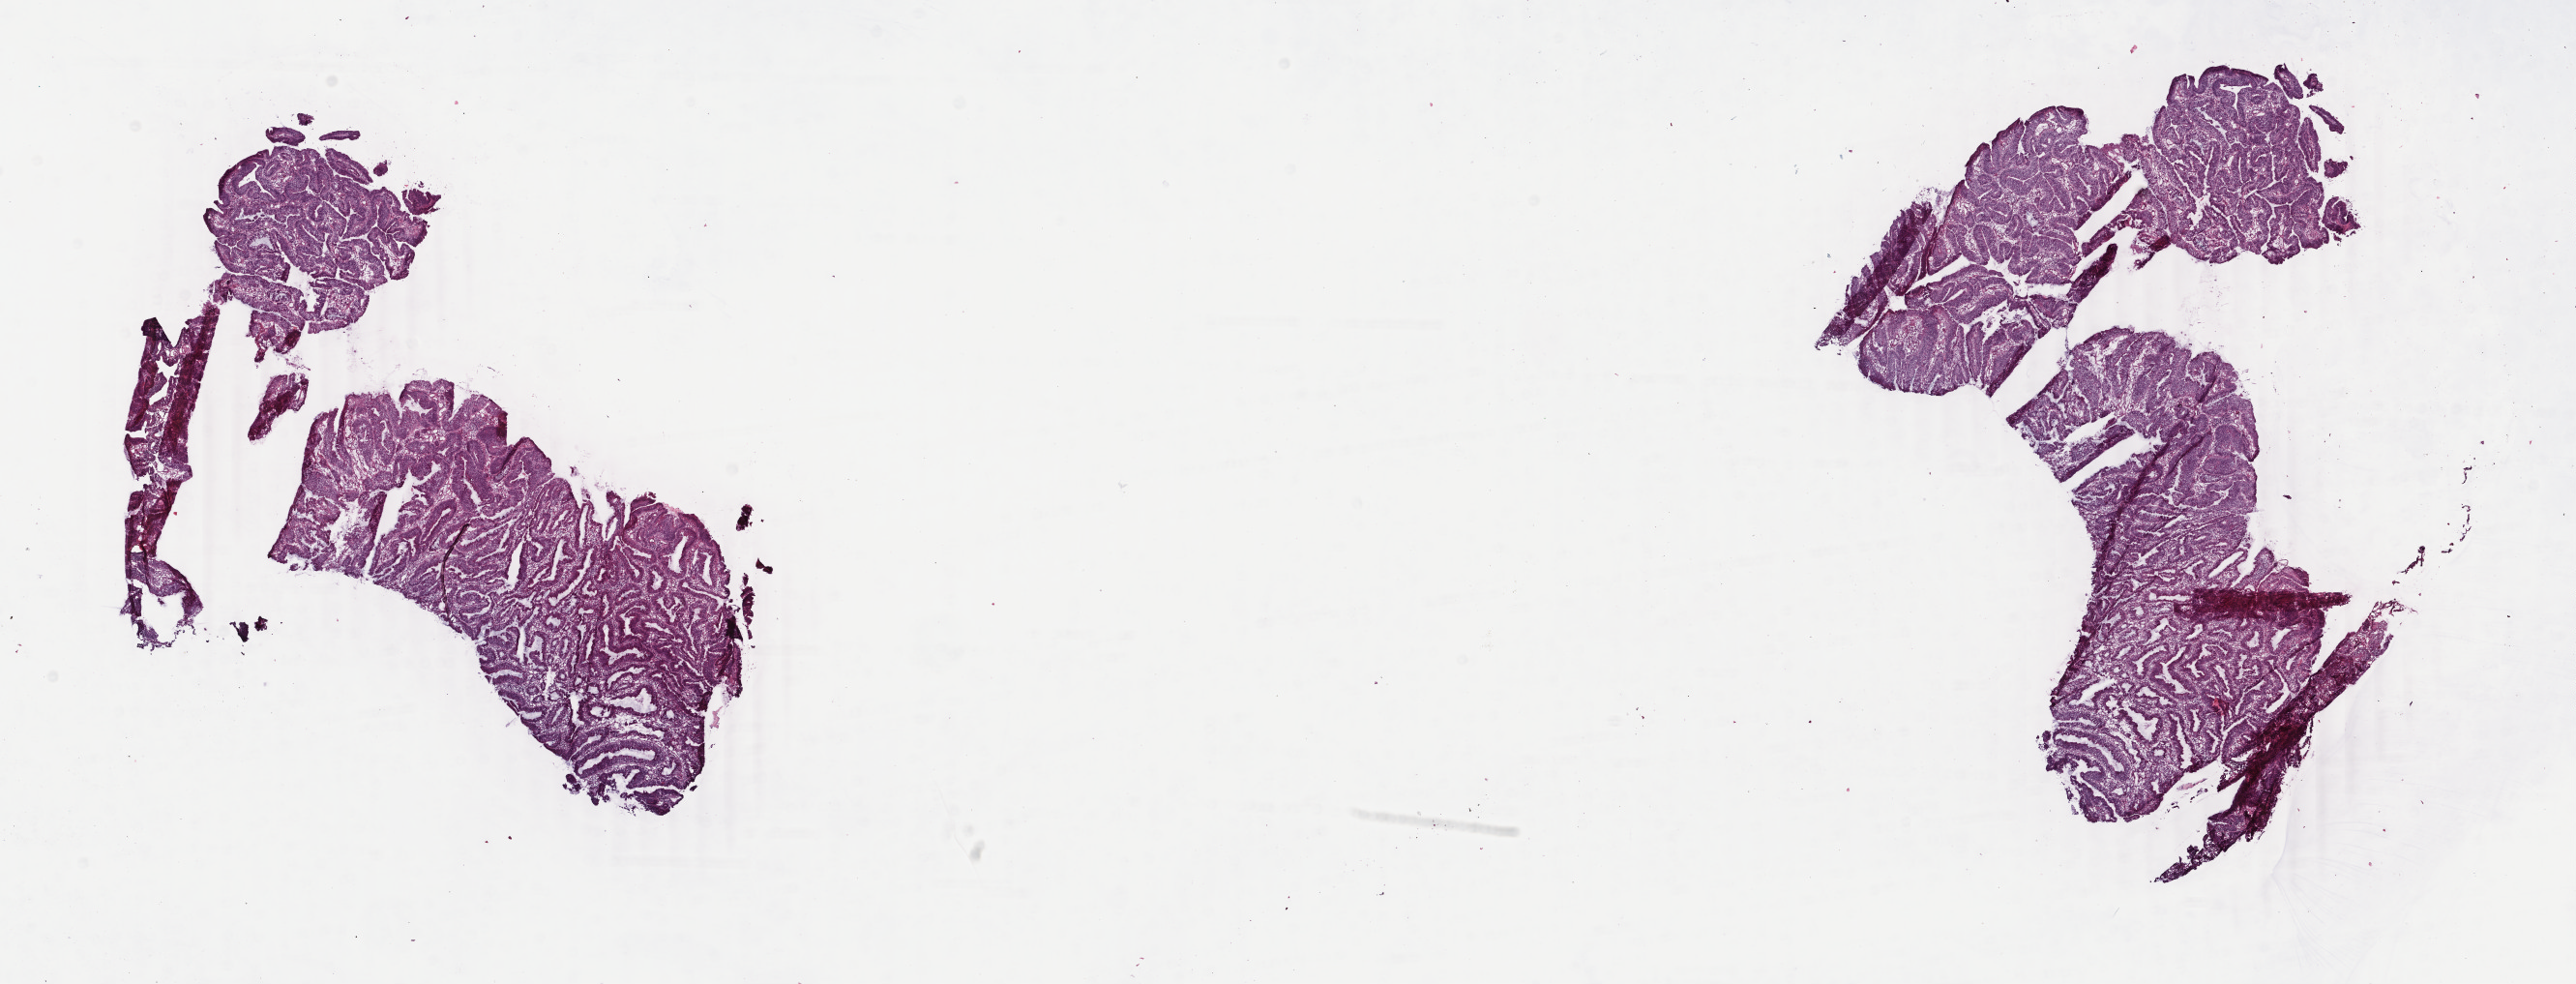
Whole-slide histology image, Hematoxylin and eosin (H&E) stained — shown as a low-resolution overview of the whole scanned area (about 21.2 x 8.1 mm), frozen section, primary tumour sample from the rectum. Female patient; age at initial diagnosis 64 years.
Histologic diagnosis: Adenocarcinoma, NOS.